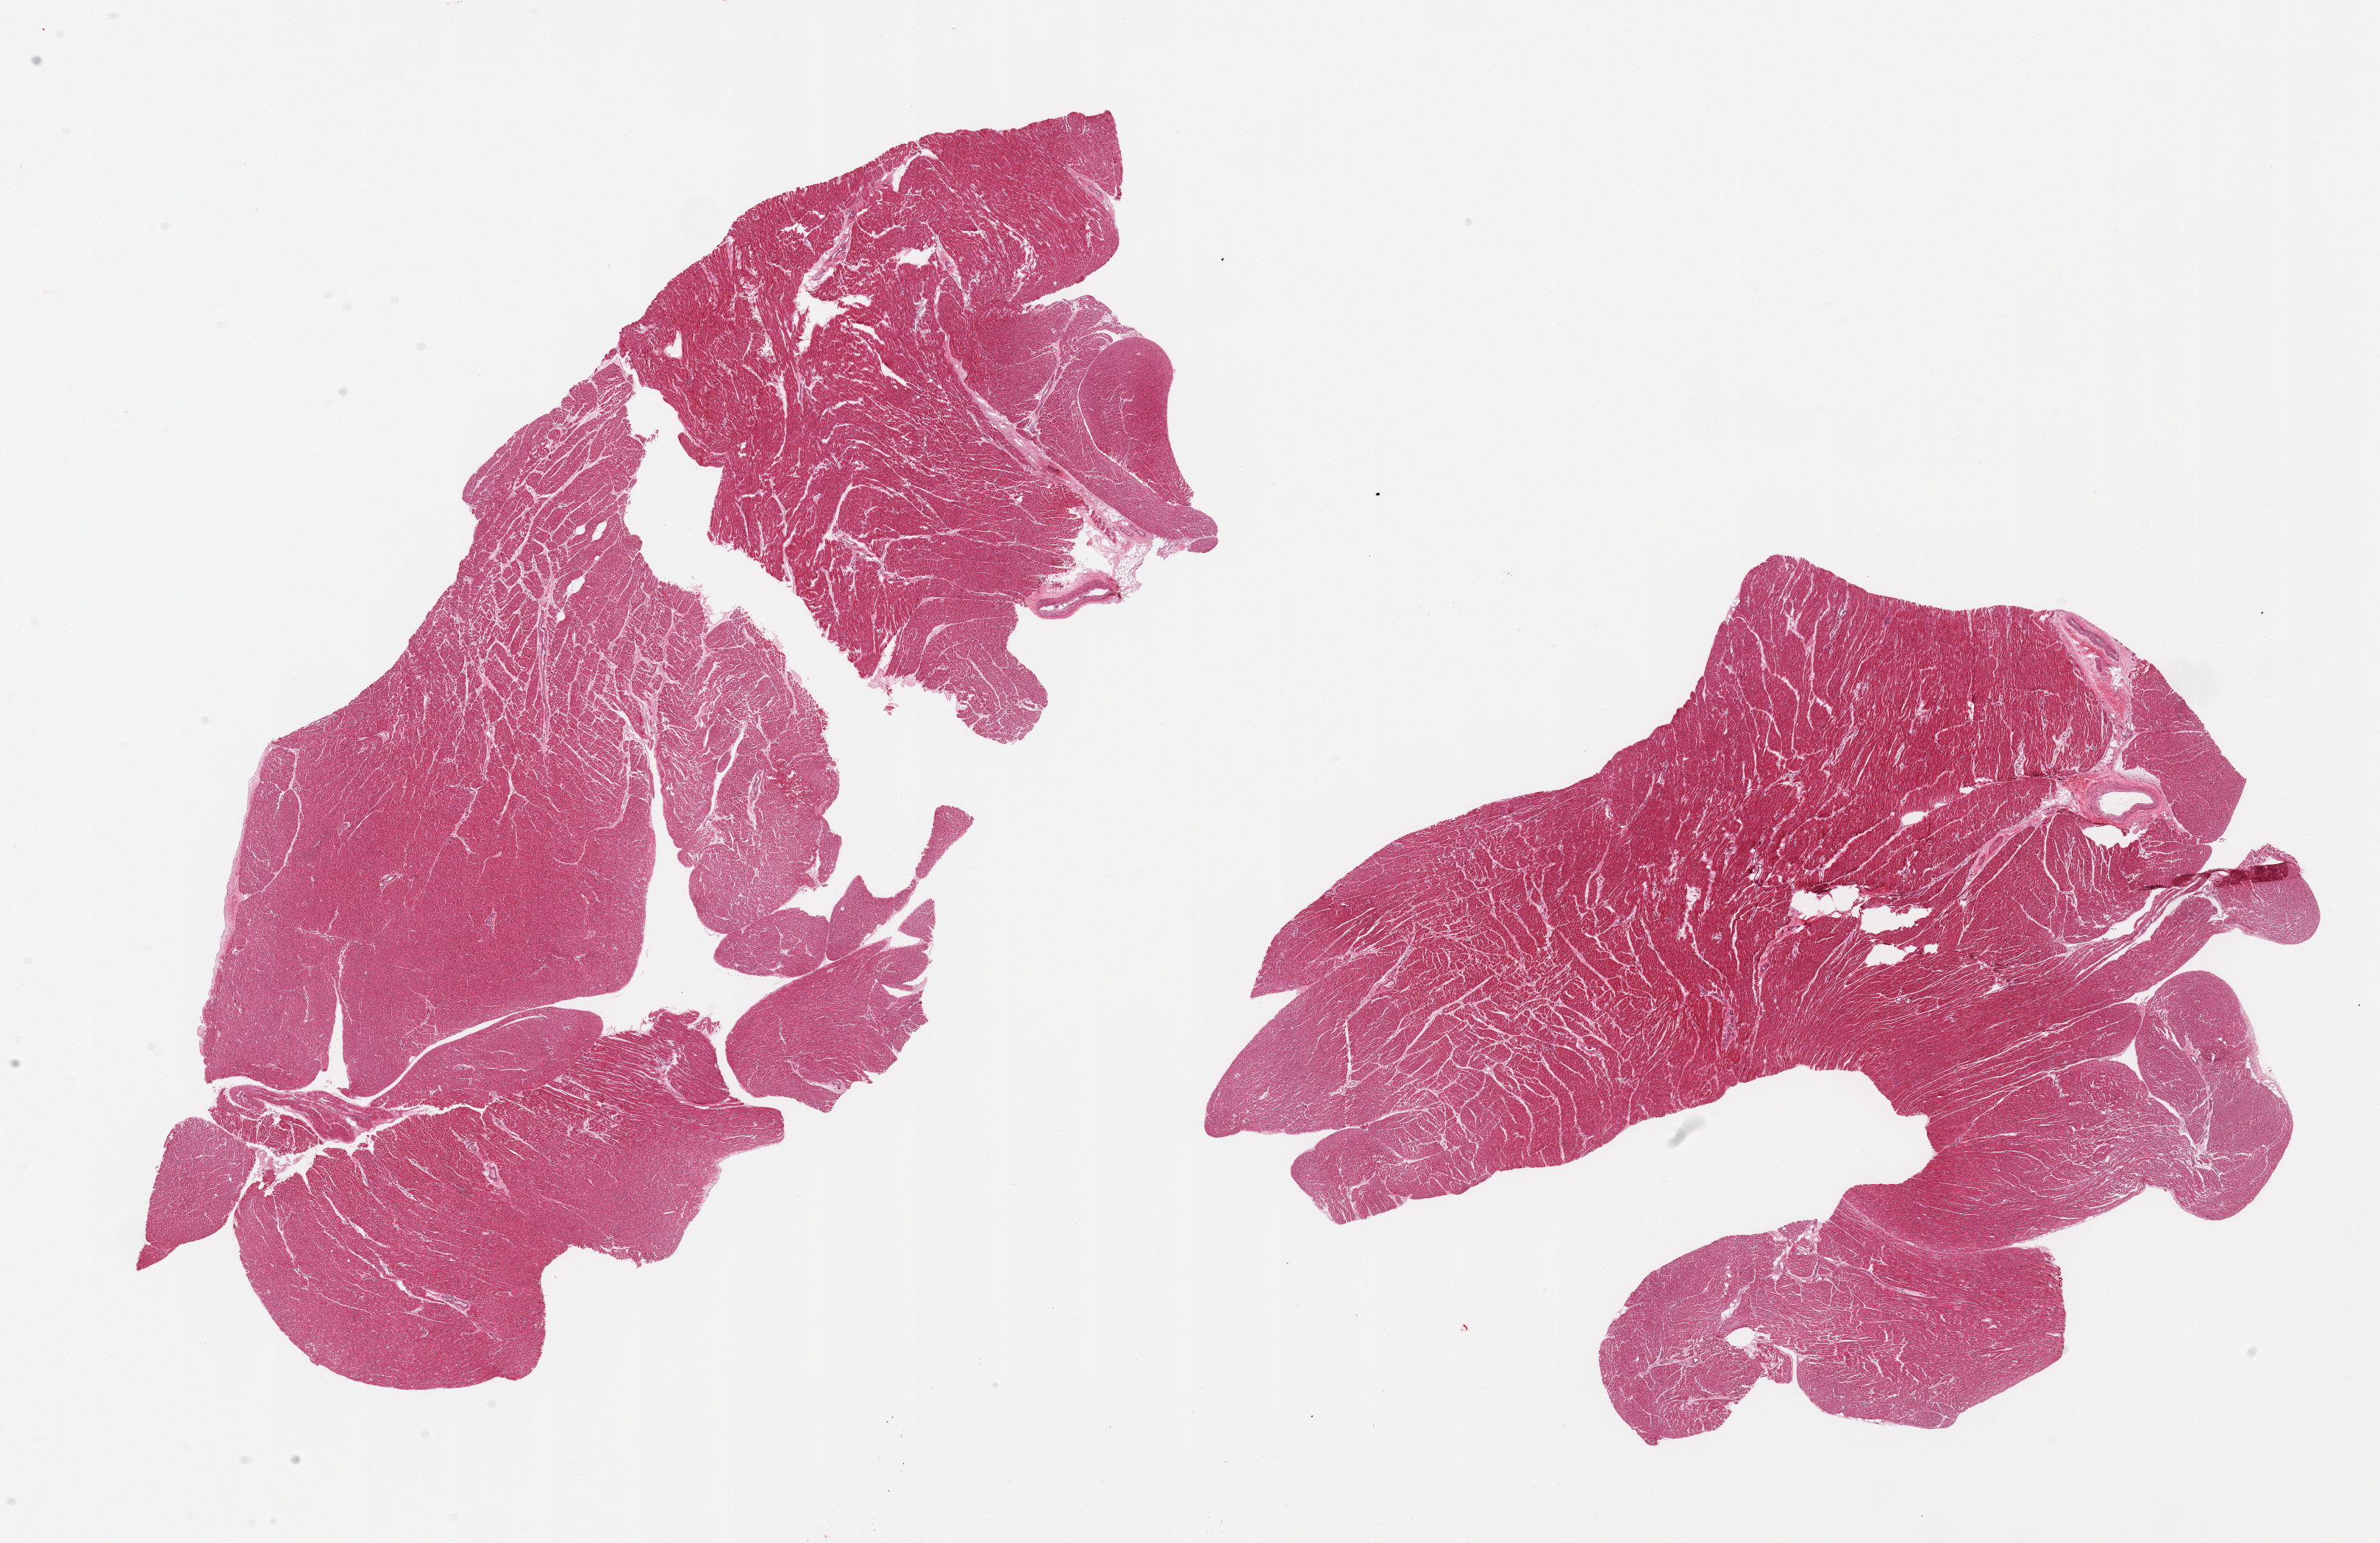
Whole-slide image, haematoxylin and eosin stain, shown as a low-resolution overview of the whole scanned area (about 25.6 x 16.6 mm); PAXgene-fixed, paraffin-embedded tissue; target tissue: heart; donor tissue sample. Donor sex: female.
• reviewer comment on this tissue sample: 2 pieces